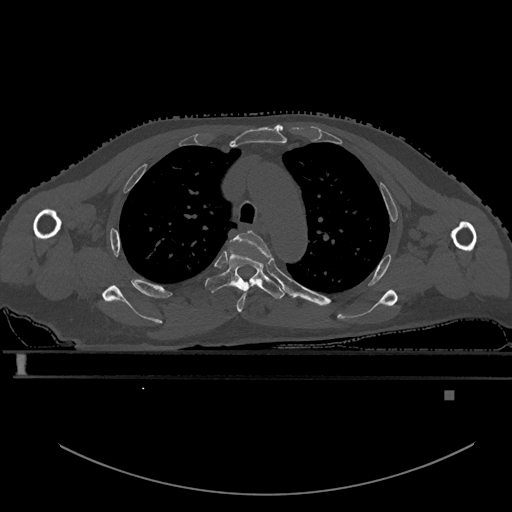
CT including the spine, one axial slice; slice 420 of 969 in the series (ordered by position); bone window (W 1800 / L 400 HU); 0.5 mm slice thickness; 512 × 512 image matrix. Patient: male, 82 years. From the clinical record (not read from this slice): primary cancer: prostate; vertebrae with lytic lesions (as recorded): T11, T9, T8, T2.
Outlined on this slice (semi-automatically segmented with operator editing):
- T3 vertebra: box from (x=234, y=230) to (x=272, y=312) px
- T4 vertebra: (x=205, y=250)–(x=285, y=299)